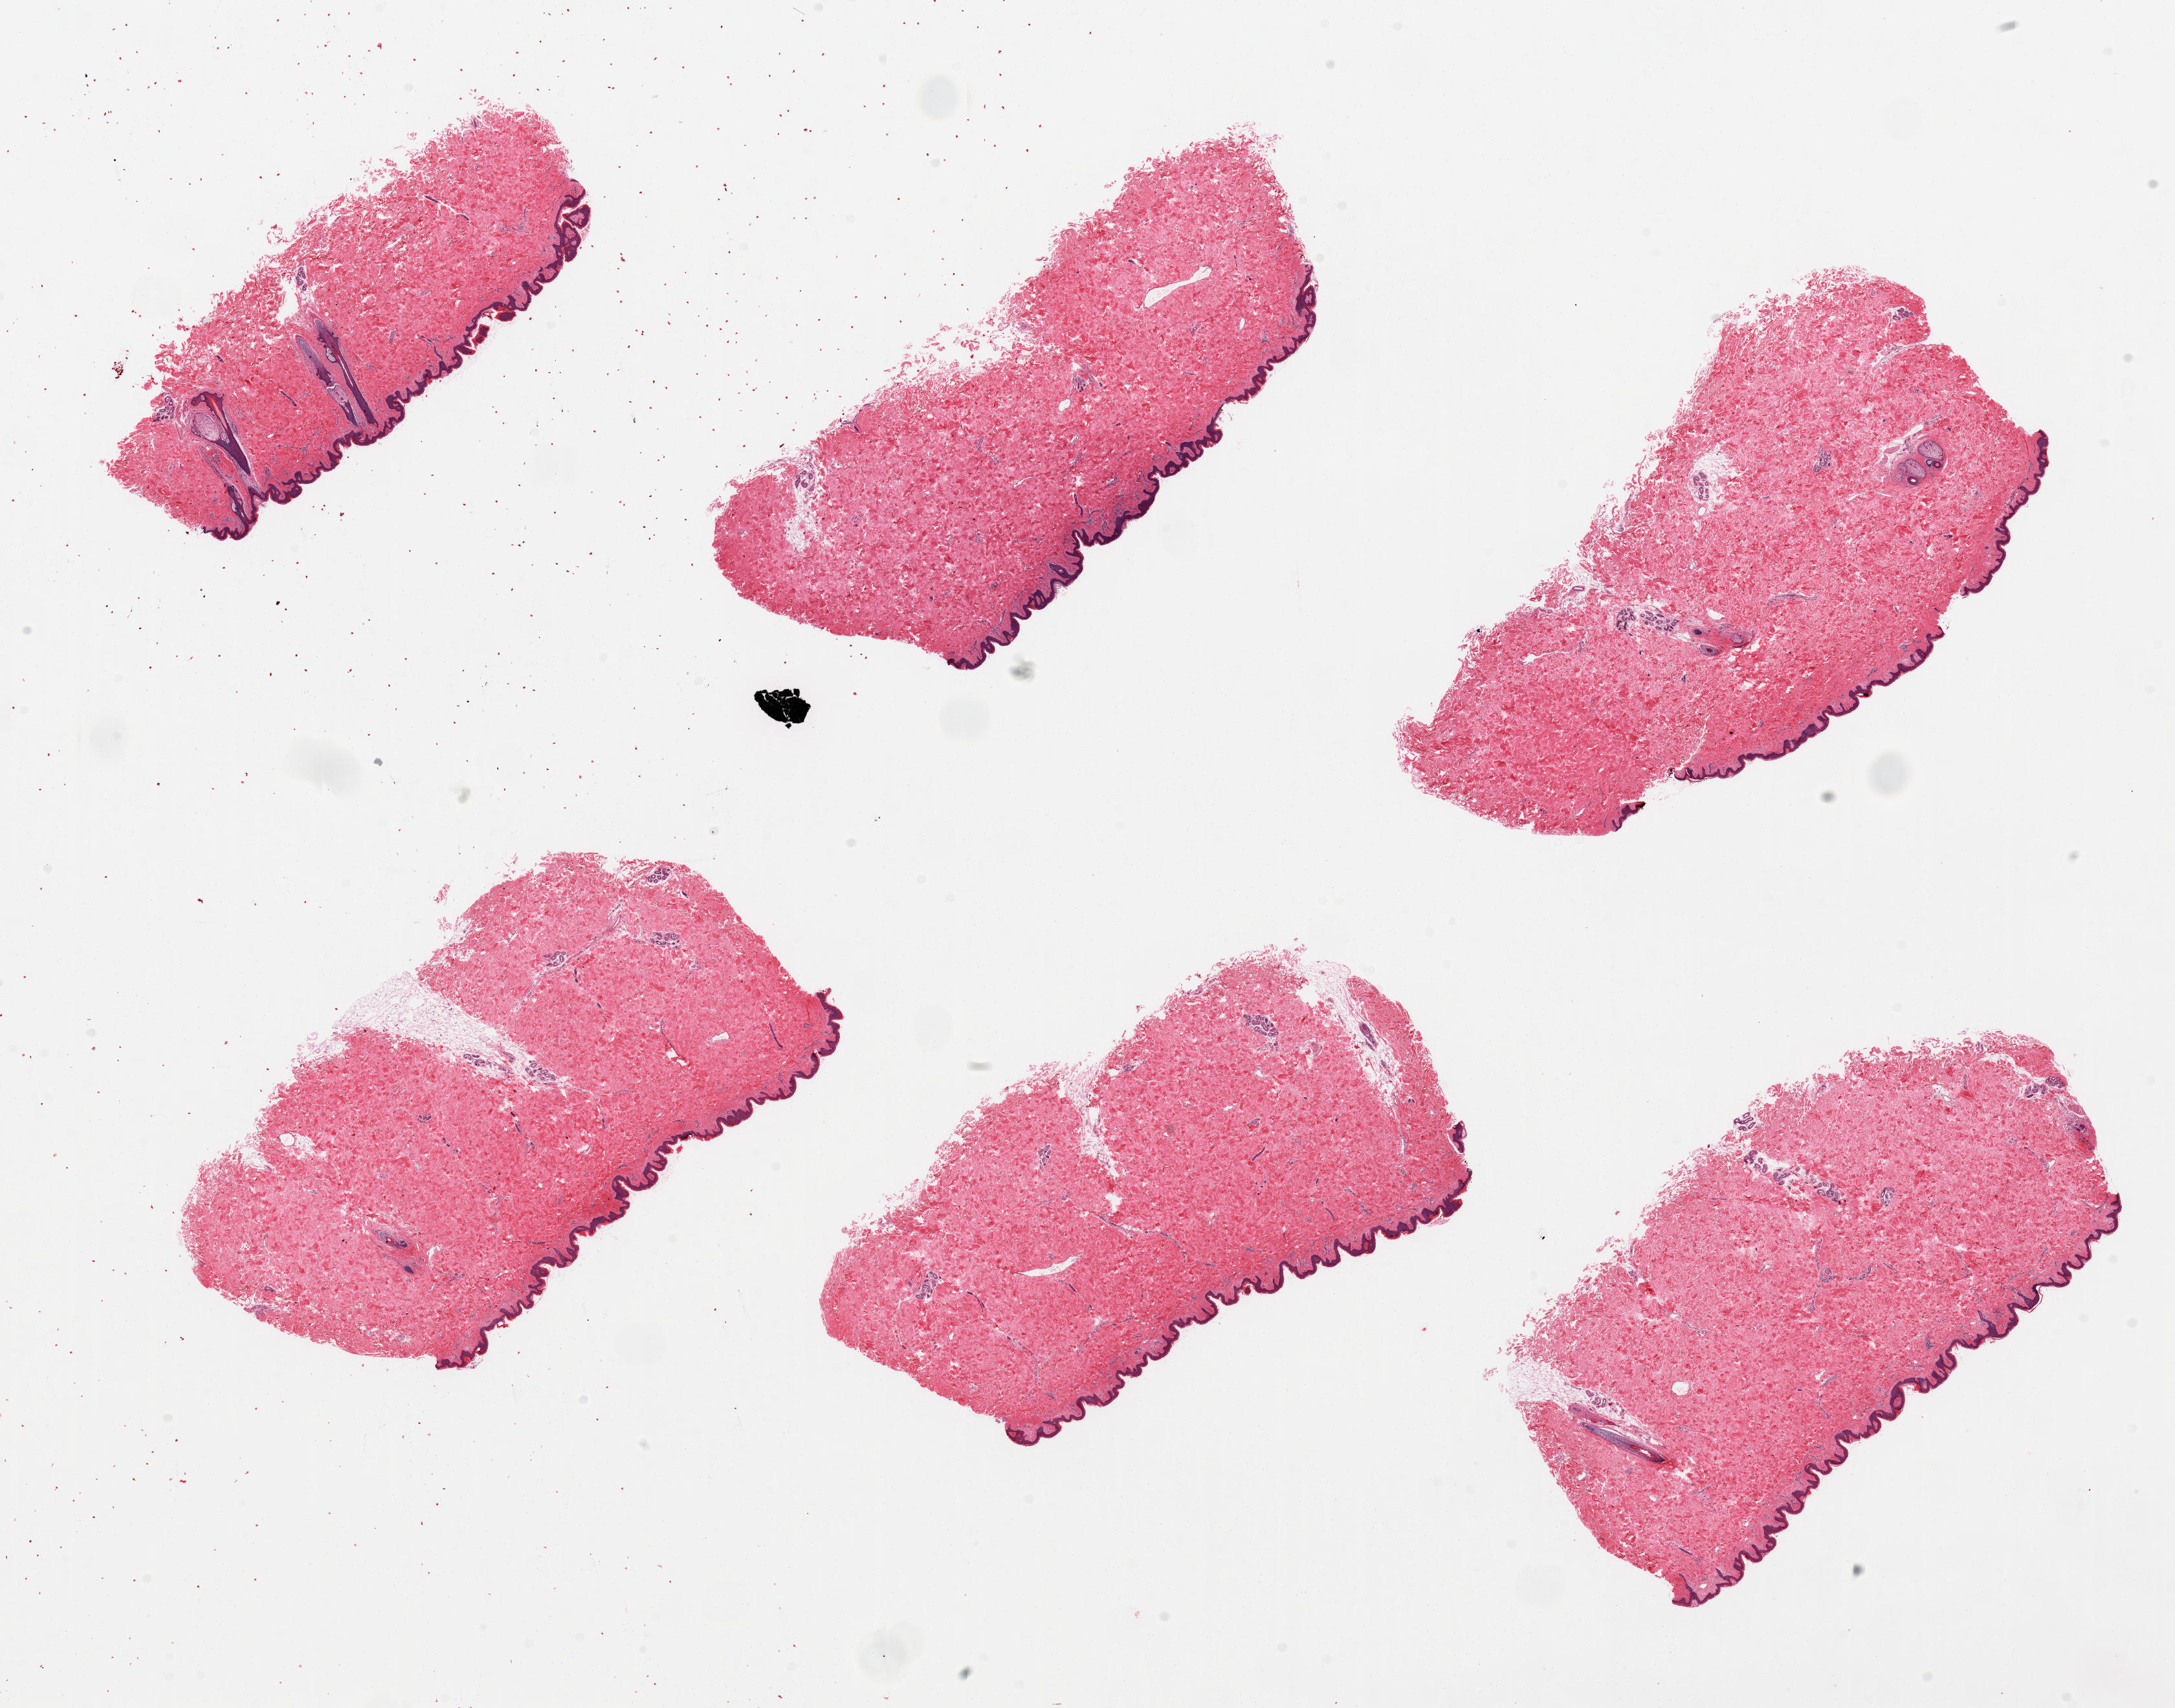
Digitized hematoxylin and eosin (H&E)-stained section, a low-resolution overview of the entire scanned area, about 26.6 x 20.9 mm (slide scanned at 20x); PAXgene-fixed paraffin-embedded (PFPE) section; sampled site (target tissue): skin of suprapubic region; donor tissue sample.
• reviewer comment on this tissue sample: 6 pieces, well trimmed with minimal internal fat